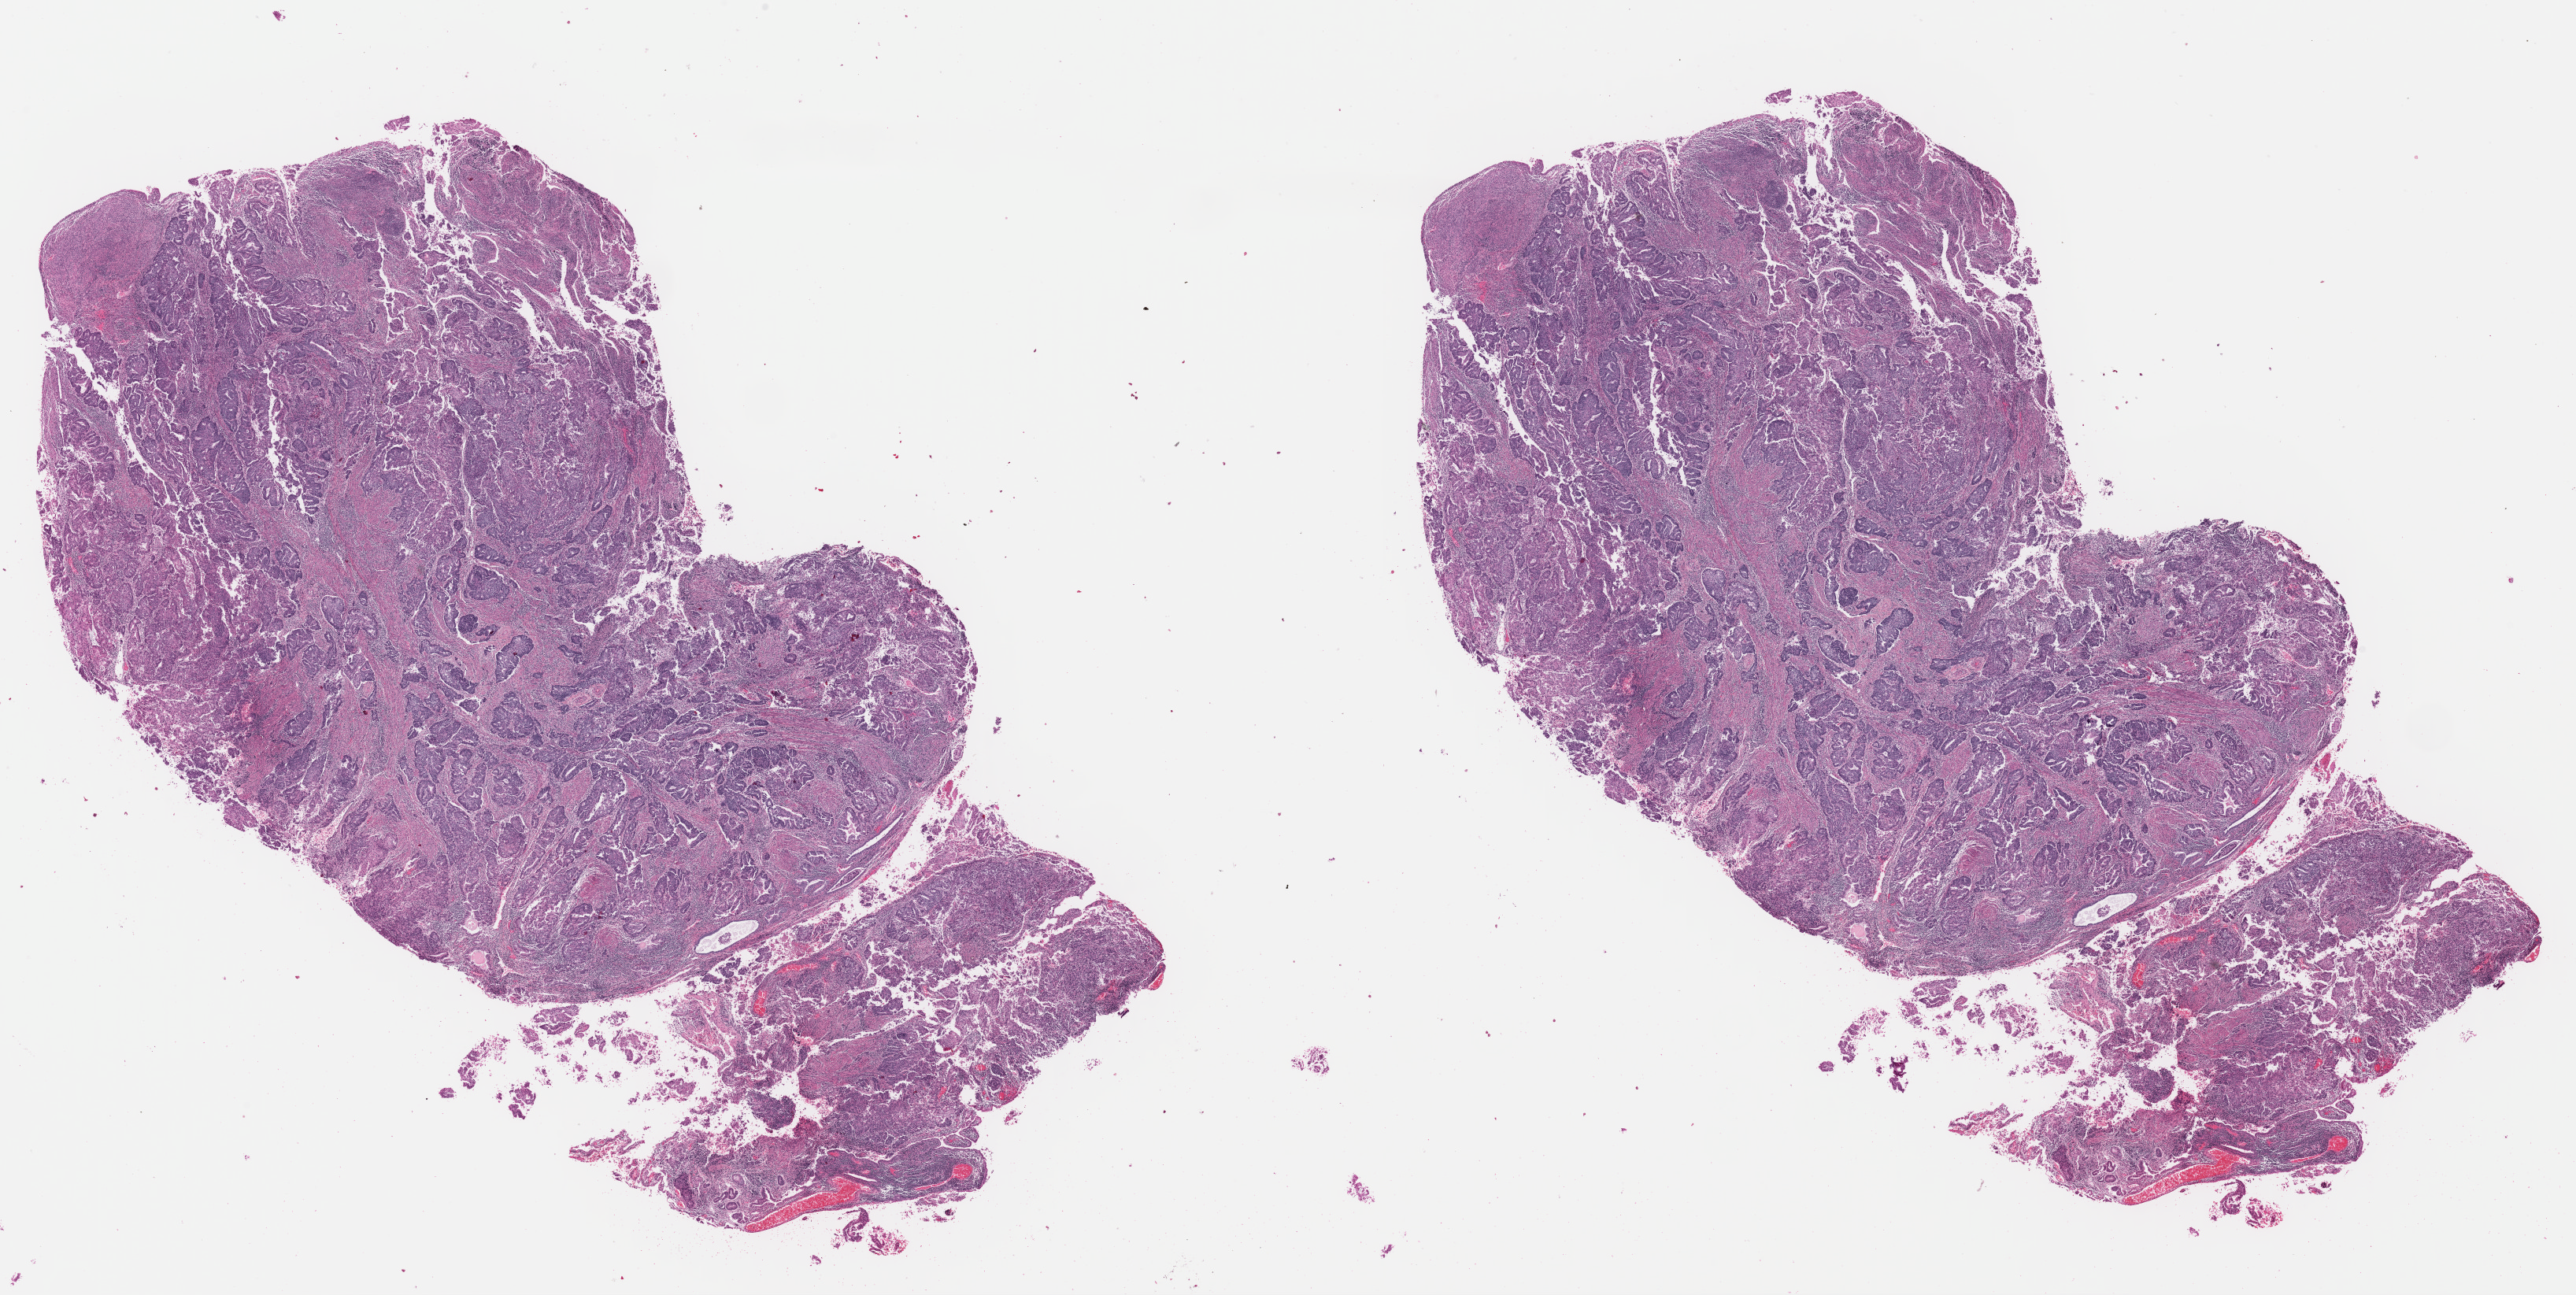
H&E-stained whole-slide image, whole scanned area (about 25.8 x 13.0 mm, acquisition: 40x scan) shown as a low-resolution overview, formalin-fixed paraffin-embedded (FFPE) diagnostic section, primary tumour sample from the uterus. Female patient; age at initial diagnosis 74 years. Histologic grade: G3 (poorly differentiated).
FIGO stage: IB. Lymph nodes positive (case pathology): 0 of 12 examined. Diagnosis: Endometrioid adenocarcinoma, NOS (endometrium).